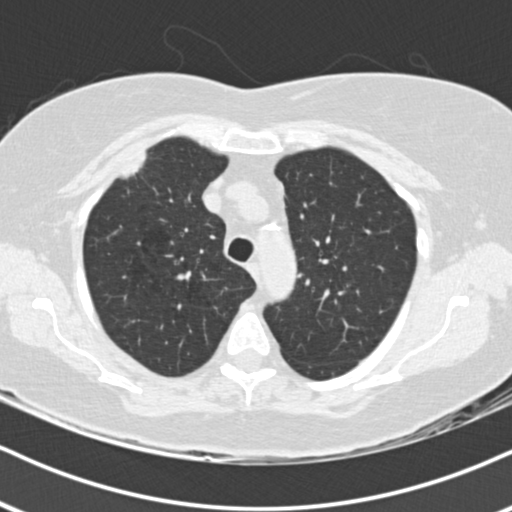
Chest CT (low-dose screening protocol), one axial image. Baseline annual screen. Lung window (W 1500 / L -600 HU). 2 mm slice thickness. Standard (soft-tissue) reconstruction kernel (B30f). Slice 40 of 178 in the series. Female, age 74 years at enrolment. Former smoker at enrolment.
• Expert-annotated lung lesion, bounding box [x1, y1, x2, y2] px = [103, 141, 163, 195].
• Reader record for this screening exam (exam-level; its link to the box is not recorded): non-calcified nodule or mass ≥4 mm, right upper lobe, 16 × 10 mm, poorly defined margins, soft tissue attenuation.
• Lung cancer was diagnosed 33 days after this screen: adenocarcinoma, NOS, right upper lobe, poorly differentiated (G3), stage IIIA (AJCC 6th edition), 24 mm at pathology.